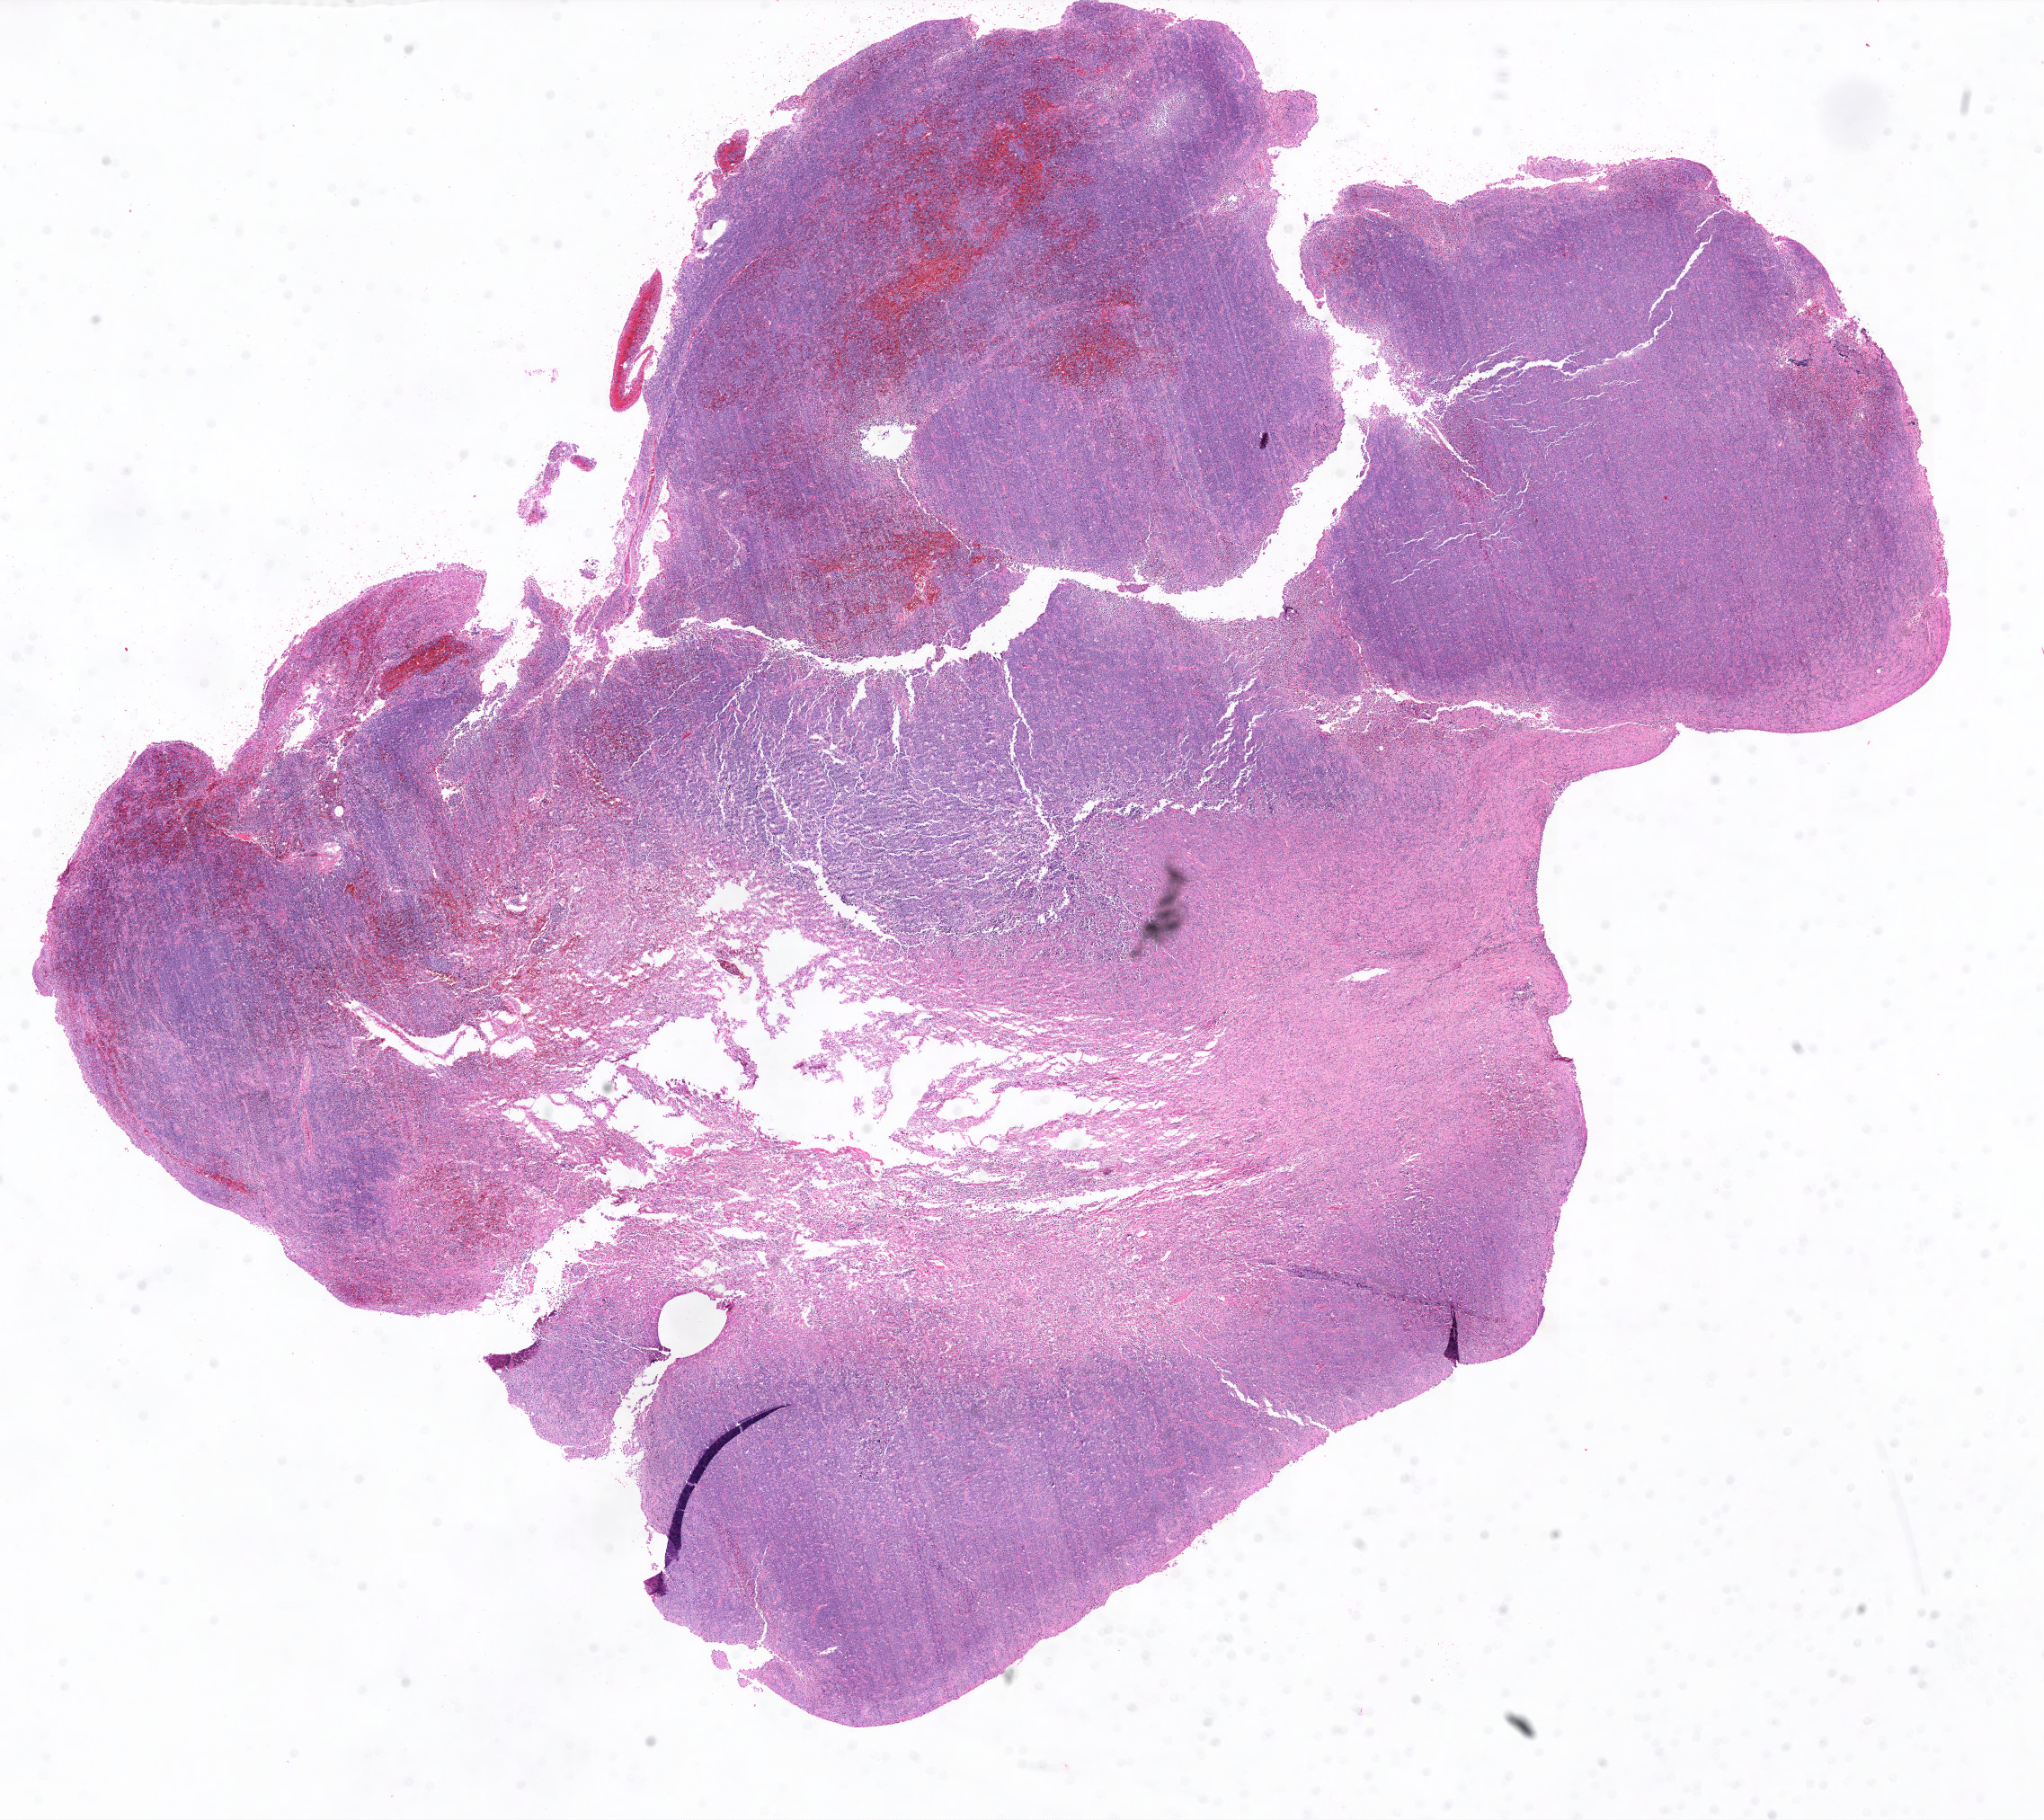
H&E-stained whole-slide image, shown as a low-resolution overview of the whole scanned area (about 16.9 x 15.1 mm), formalin-fixed paraffin-embedded (FFPE) diagnostic section, sample: primary tumour, lymphoid tissue. Female, age 66 years at initial diagnosis.
Diagnosis: Diffuse large B-cell lymphoma, NOS (lymph nodes of head, face and neck).